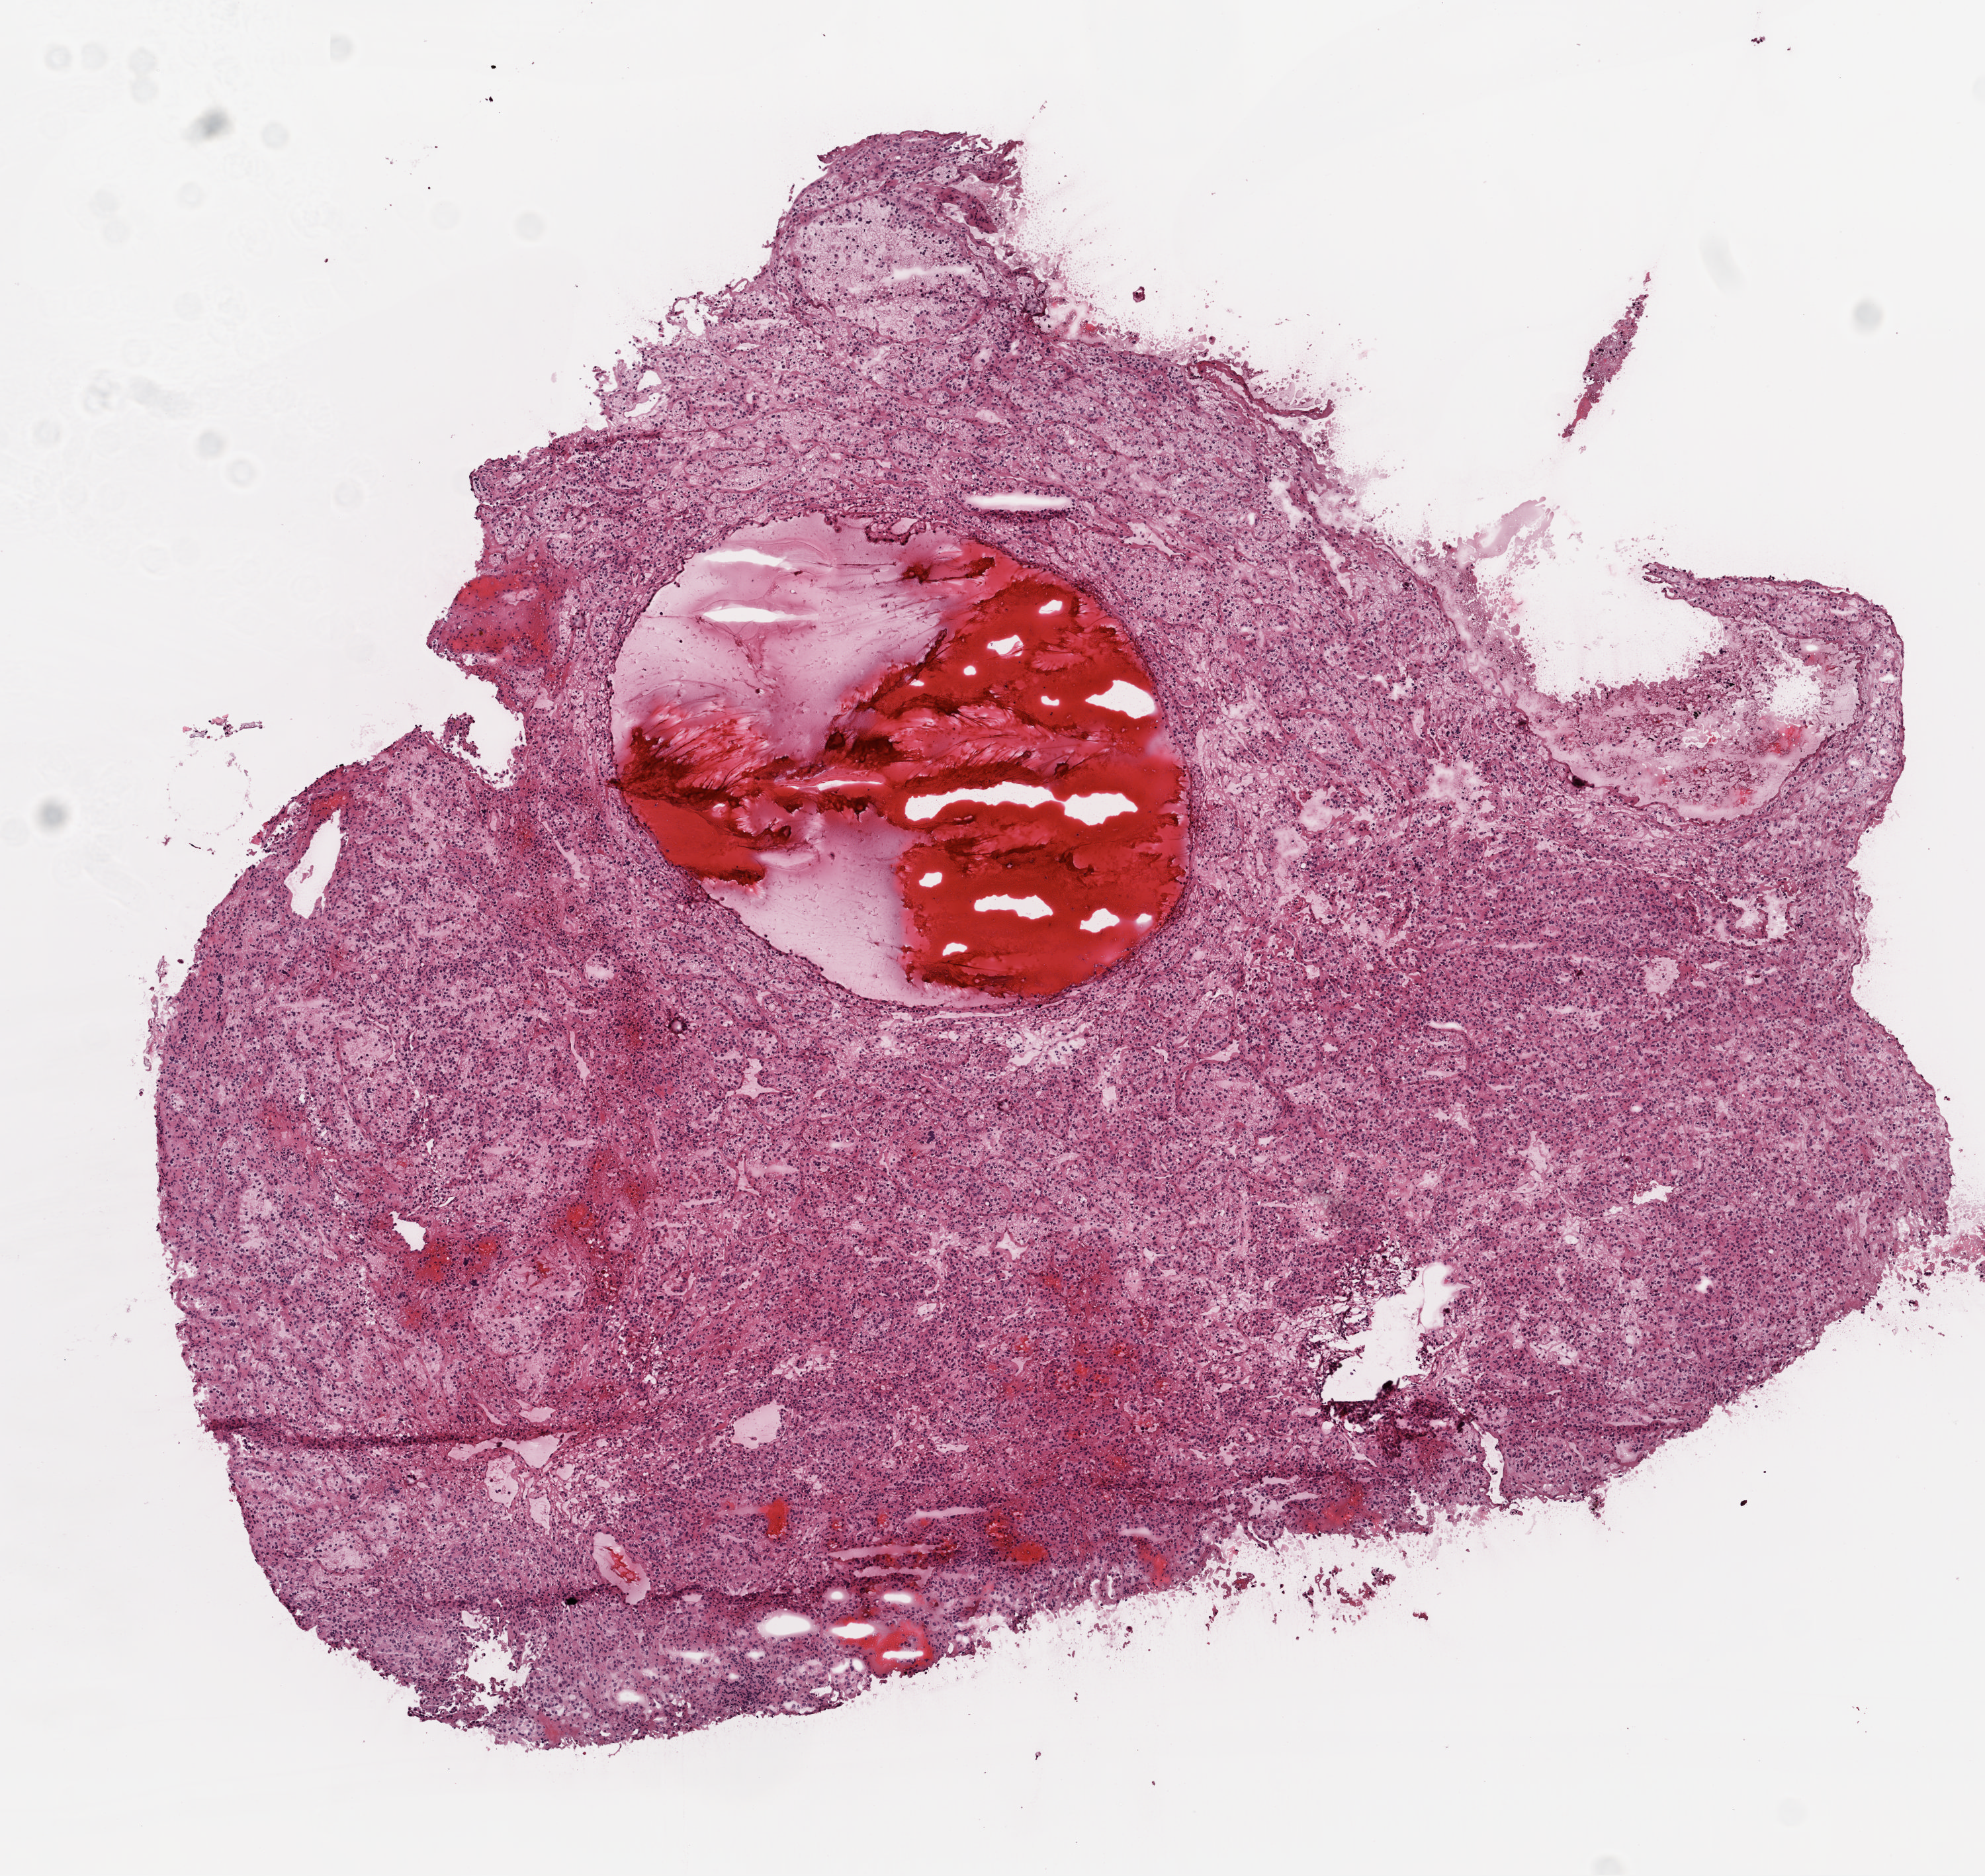
Whole-slide histology image, H&E-stained — low-resolution overview of the scanned area, about 6.0 x 5.7 mm. Frozen section. Kidney, primary tumour sample. Male, age 75 years at initial diagnosis. Histologic grade: G2 (moderately differentiated). Composition of this section per pathologist review: tumour cells 90%, tumour nuclei 90%, normal cells 0%, stromal cells 10%, necrosis 0%.
Histologic diagnosis: Clear cell adenocarcinoma, NOS. AJCC pathologic stage: I.